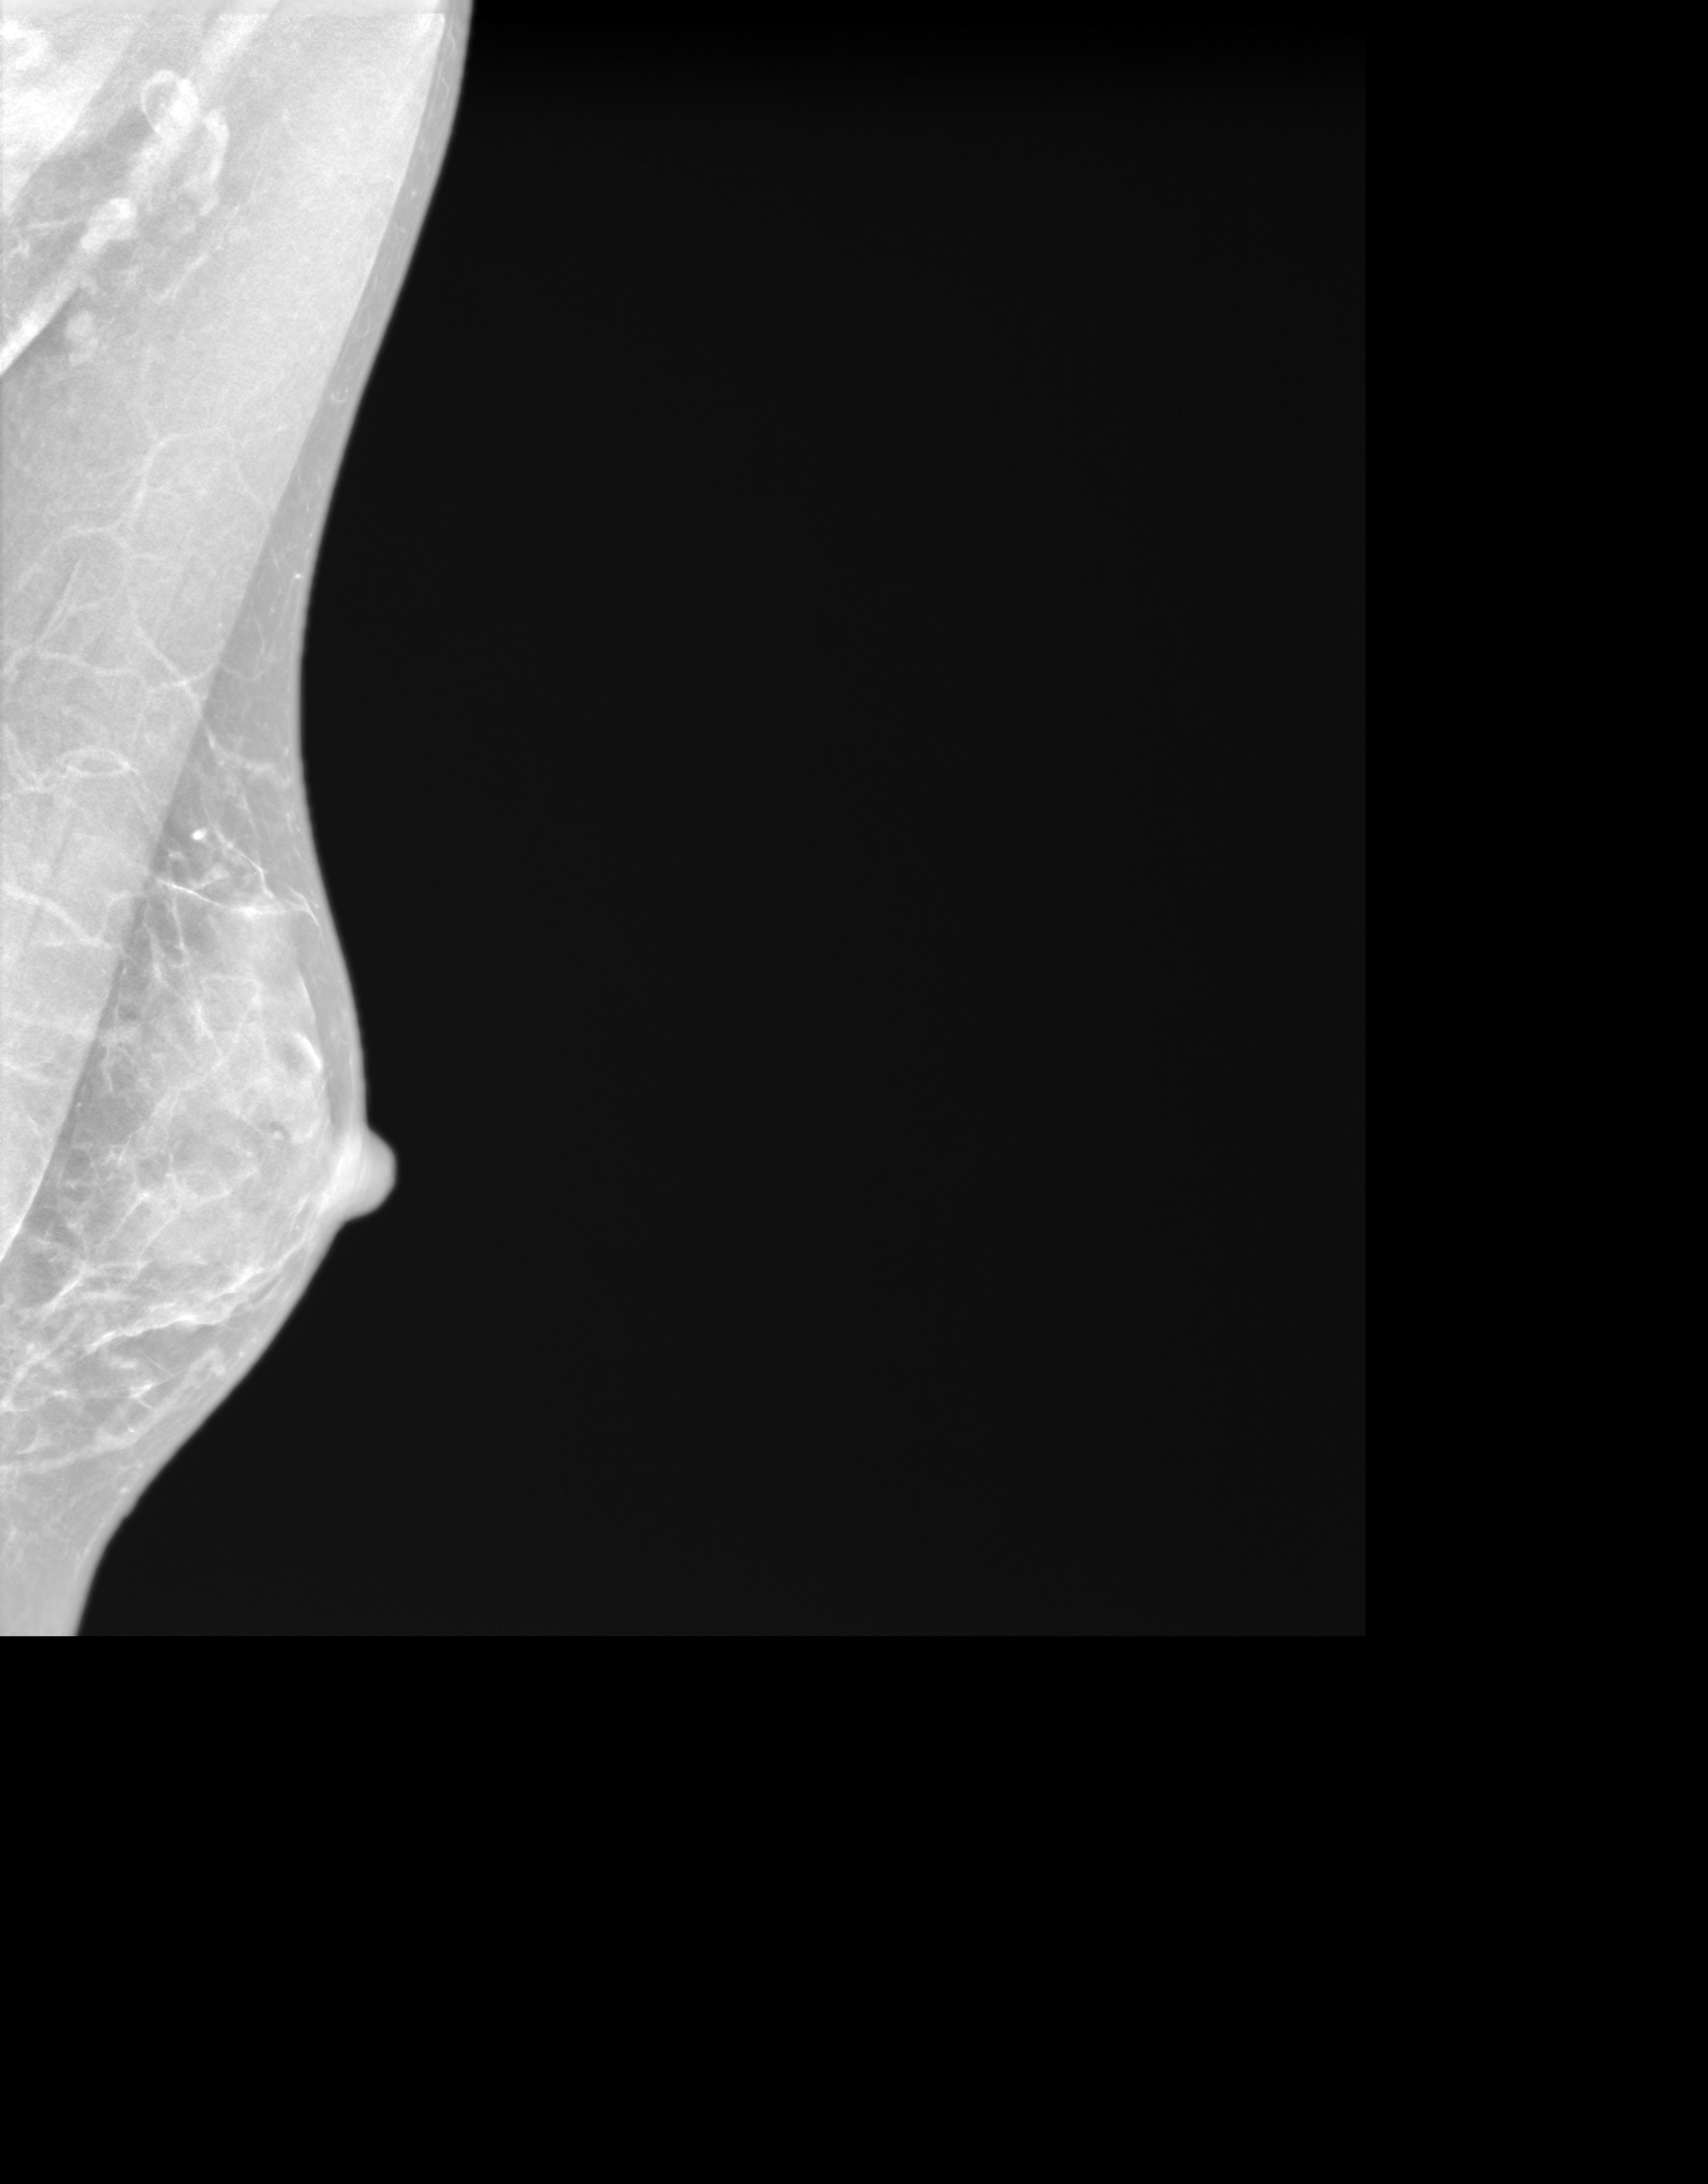
Annual screening mammography examination, system: SenoIris_1SP2(440). Patient: female, 56 years.
Image type: synthesized 2-D view from tomosynthesis. Breast: left. Projection: MLO view.